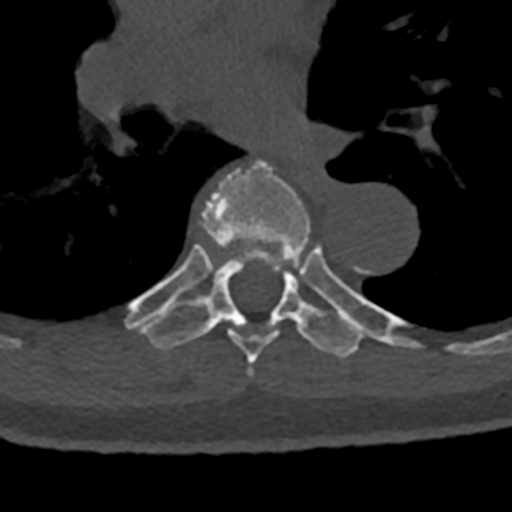
CT including the spine, one axial slice; slice 784 of 797 in the series (ordered by position); reconstruction kernel Br40s/3; bone window (W 1800 / L 400 HU); 0.5 mm slice thickness; 512 × 512 image matrix, field of view 160 × 160 mm. Patient: male, 74 years. From the clinical record (not read from this slice): primary cancer: renal; vertebrae with lytic lesions (as recorded): T10, L1, L2, L3, L4, L5.
Annotated regions visible in this slice (semi-automatically segmented with operator editing):
- T6 vertebra: bounding box (x1, y1, x2, y2) in pixels: (169, 159, 311, 376)
- T7 vertebra: (126, 245, 414, 359)